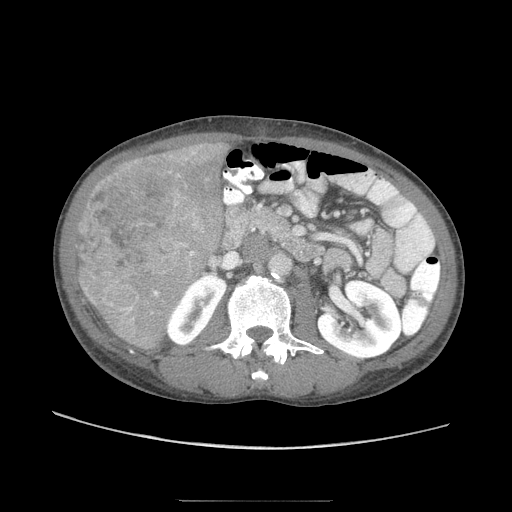
Contrast-enhanced abdominal CT (liver protocol), one axial slice; slice 24 of 103 in the series (ordered by position); 120 kVp; soft-tissue window (W 400 / L 40 HU); 2.5 mm slice thickness; 512 × 512 image matrix, field of view 380 × 380 mm. Case-level facts recorded for this patient, not image findings: diagnosis: hepatocellular carcinoma (patient treated with transarterial chemoembolisation; whether this scan precedes or follows treatment is not stated here); TNM stage (as recorded): Stage-IIIA.
Annotated regions visible in this slice (semi-automatic segmentation, software-assisted and operator-edited):
- liver parenchyma outside the tumour (the mass and vessels are separate outlines, so this box may not span the whole liver): box from (x=80, y=136) to (x=235, y=350) px
- mass: (x=73, y=155)–(x=204, y=316)